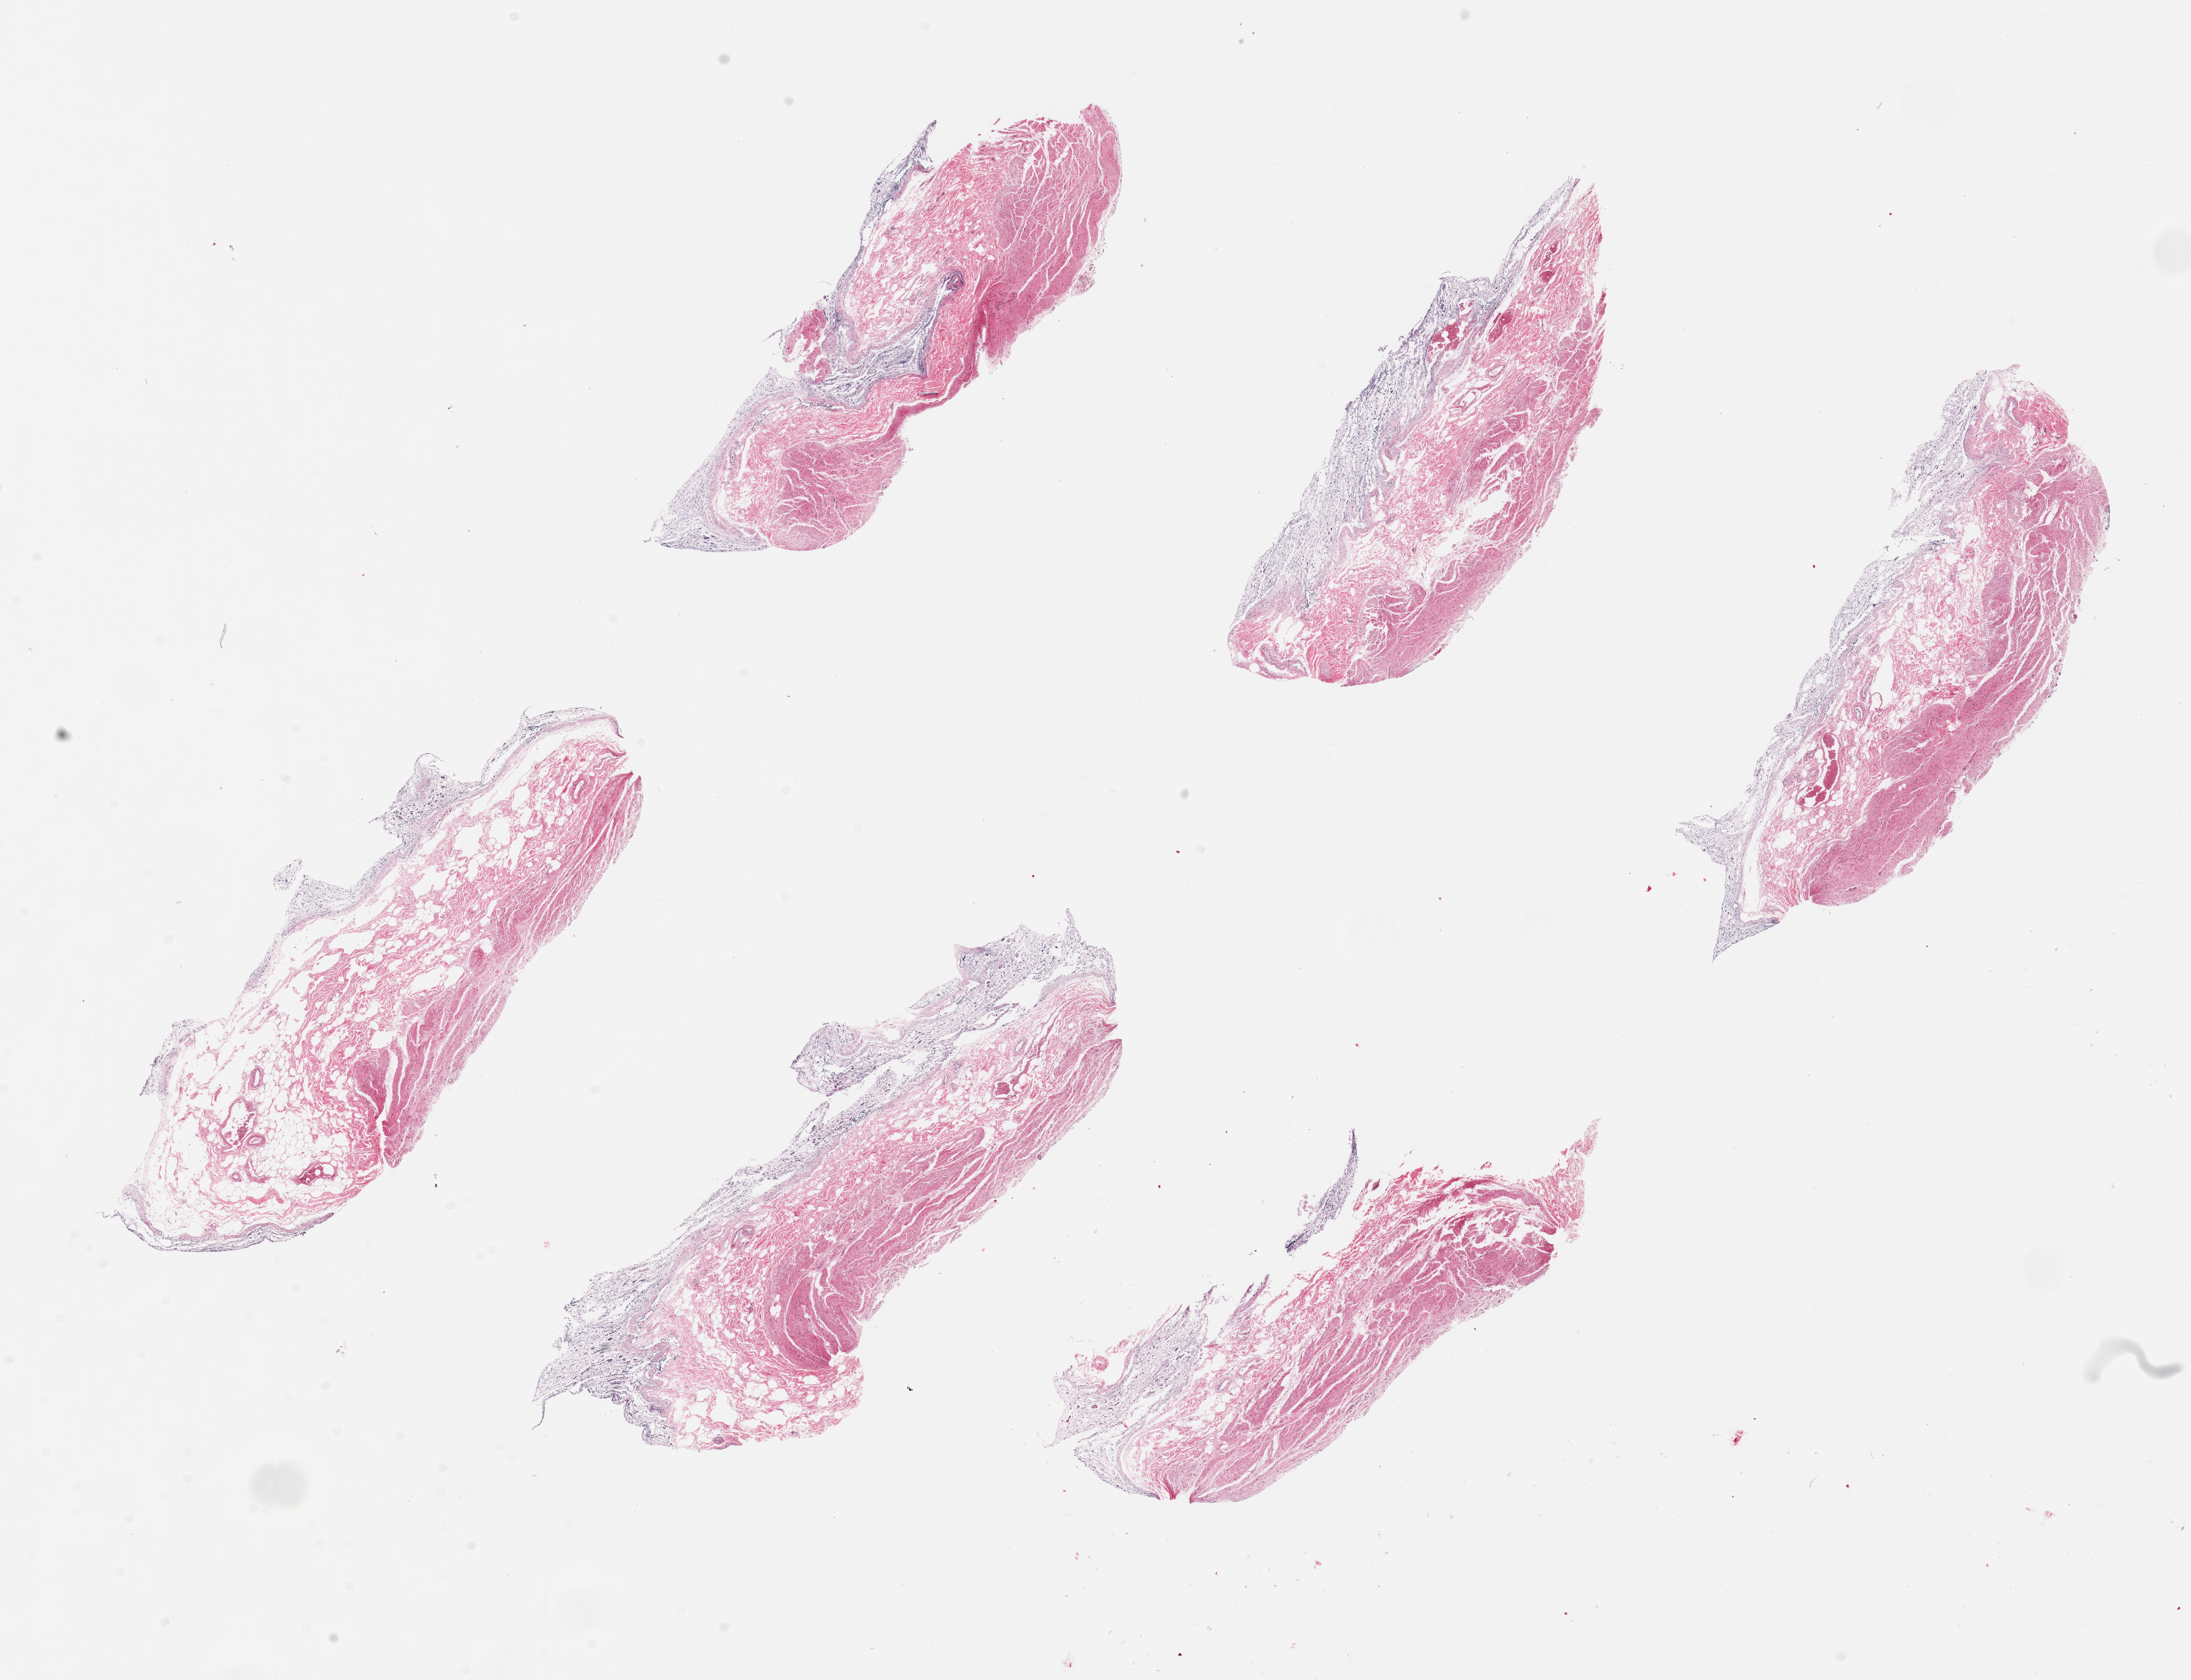
Haematoxylin and eosin whole-slide image — shown as a low-resolution overview of the whole scanned area (about 23.6 x 18.1 mm). PAXgene-fixed, paraffin-embedded tissue. Section of stomach (target tissue). Tissue donor sample. Donor sex: male.
Pathologist's review note for this sample: 6 pieces, ~7x2mm. Mucoas toally autolyzed and/or sloughed.